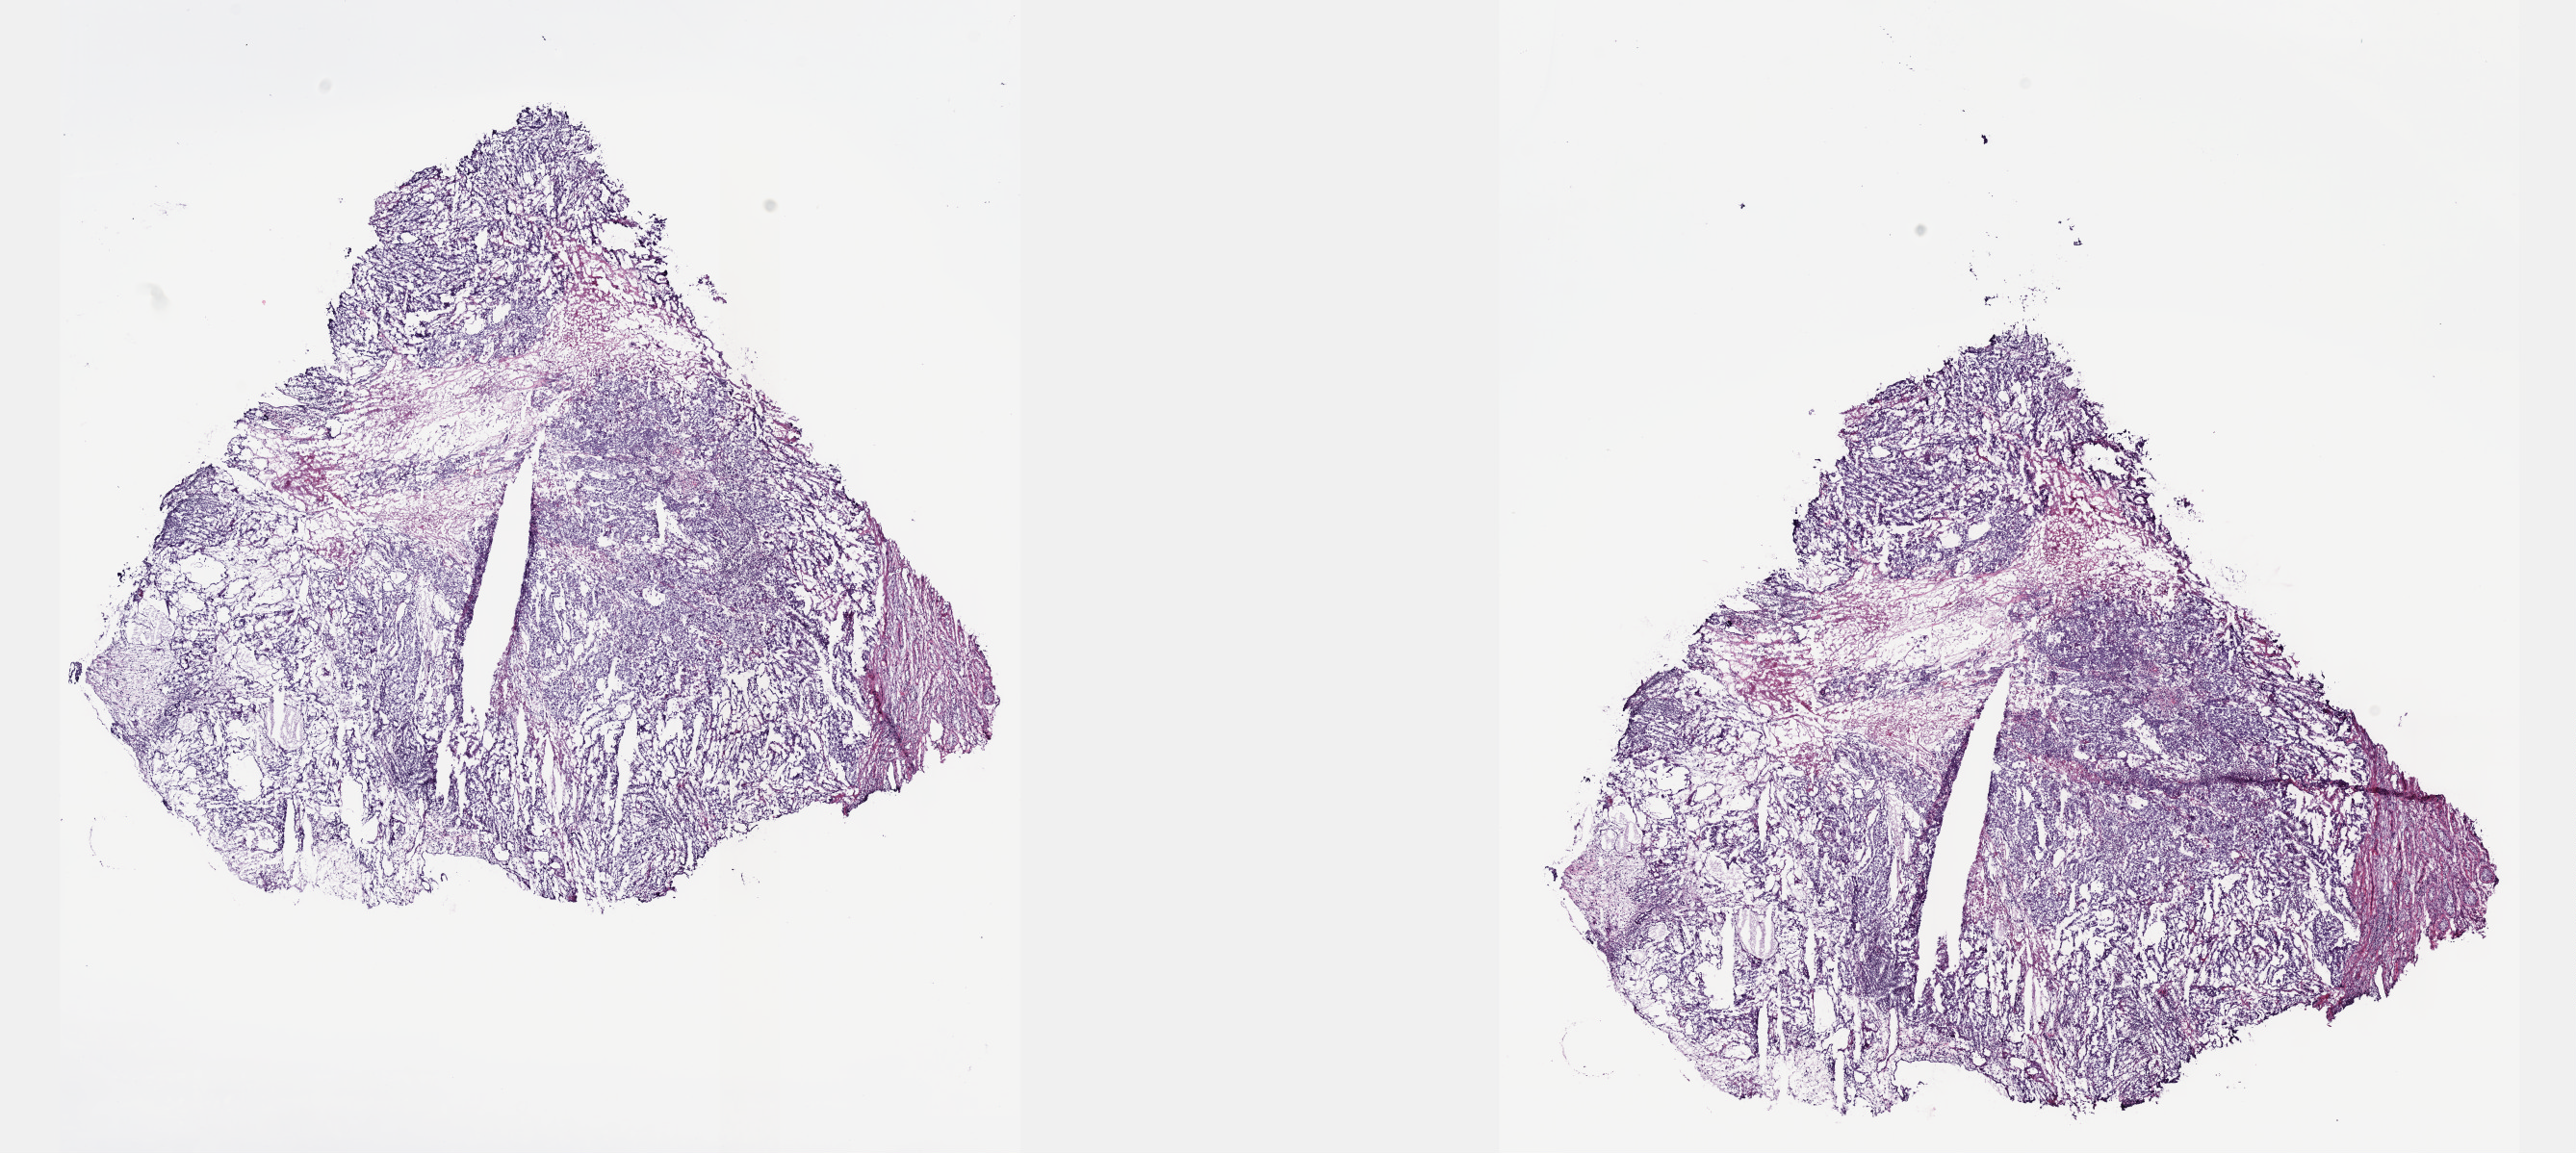
Whole-slide histology image, Hematoxylin and eosin (H&E) stained — low-resolution overview of the scanned area, about 21.6 x 9.7 mm (slide scanned at 40x); frozen section from the top of the tissue portion; testis, primary tumour sample. Patient: male, age at initial diagnosis 20 years. Slide review estimates, as recorded: tumour cells 80%, tumour nuclei 80%, normal cells 0%, stromal cells 5%, necrosis 15%. Inflammatory infiltration, as recorded: lymphocyte infiltration 40%, monocyte infiltration 20%, neutrophil infiltration 20%.
• TNM: T2 N0 M0
• pathologic diagnosis: Mixed germ cell tumor
• AJCC pathologic stage: IS (6th edition)
• laterality: left